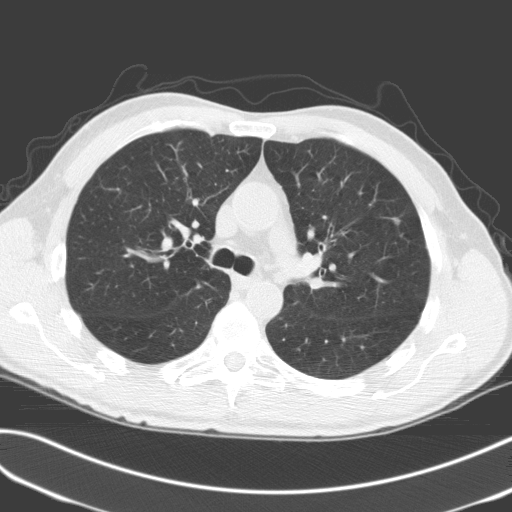
Axial slice from a low-dose chest CT screening exam; third annual screen; lung window (W 1500 / L -600 HU); 3.2 mm slice thickness; standard (soft-tissue) reconstruction kernel (C); slice 61 of 170 in the series. Male, age 68 years at enrolment. Former smoker at enrolment.
Expert-annotated lung lesion, bounding box (x1, y1, x2, y2) in pixels: (377, 202, 418, 236). Reader record for this screening exam (exam-level; its link to the box is not recorded): non-calcified nodule or mass ≥4 mm, left upper lobe, 9 × 7 mm, poorly defined margins, mixed attenuation, pre-existing on the prior screen: no. Official screen result: positive, other. Later outcome: lung cancer diagnosed 364 days after this screen — adenocarcinoma, NOS, left upper lobe, moderately differentiated (G2), stage IA (AJCC 6th edition), 6 mm at pathology.